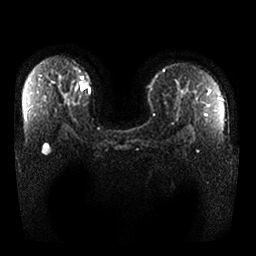
Breast MRI, one axial slice. Slice 21 of 25 in the series (ordered by position). Diffusion-weighted series; image 2 of 4 stored at this slice position (different b-values; order by instance number). 1.5 T. 4 mm slice thickness. 256 × 256 image matrix. Female patient.
Annotated regions visible in this slice (expert manual segmentation):
- tumour on diffusion-weighted imaging: bounding box [x1, y1, x2, y2] px = [81, 83, 87, 90]